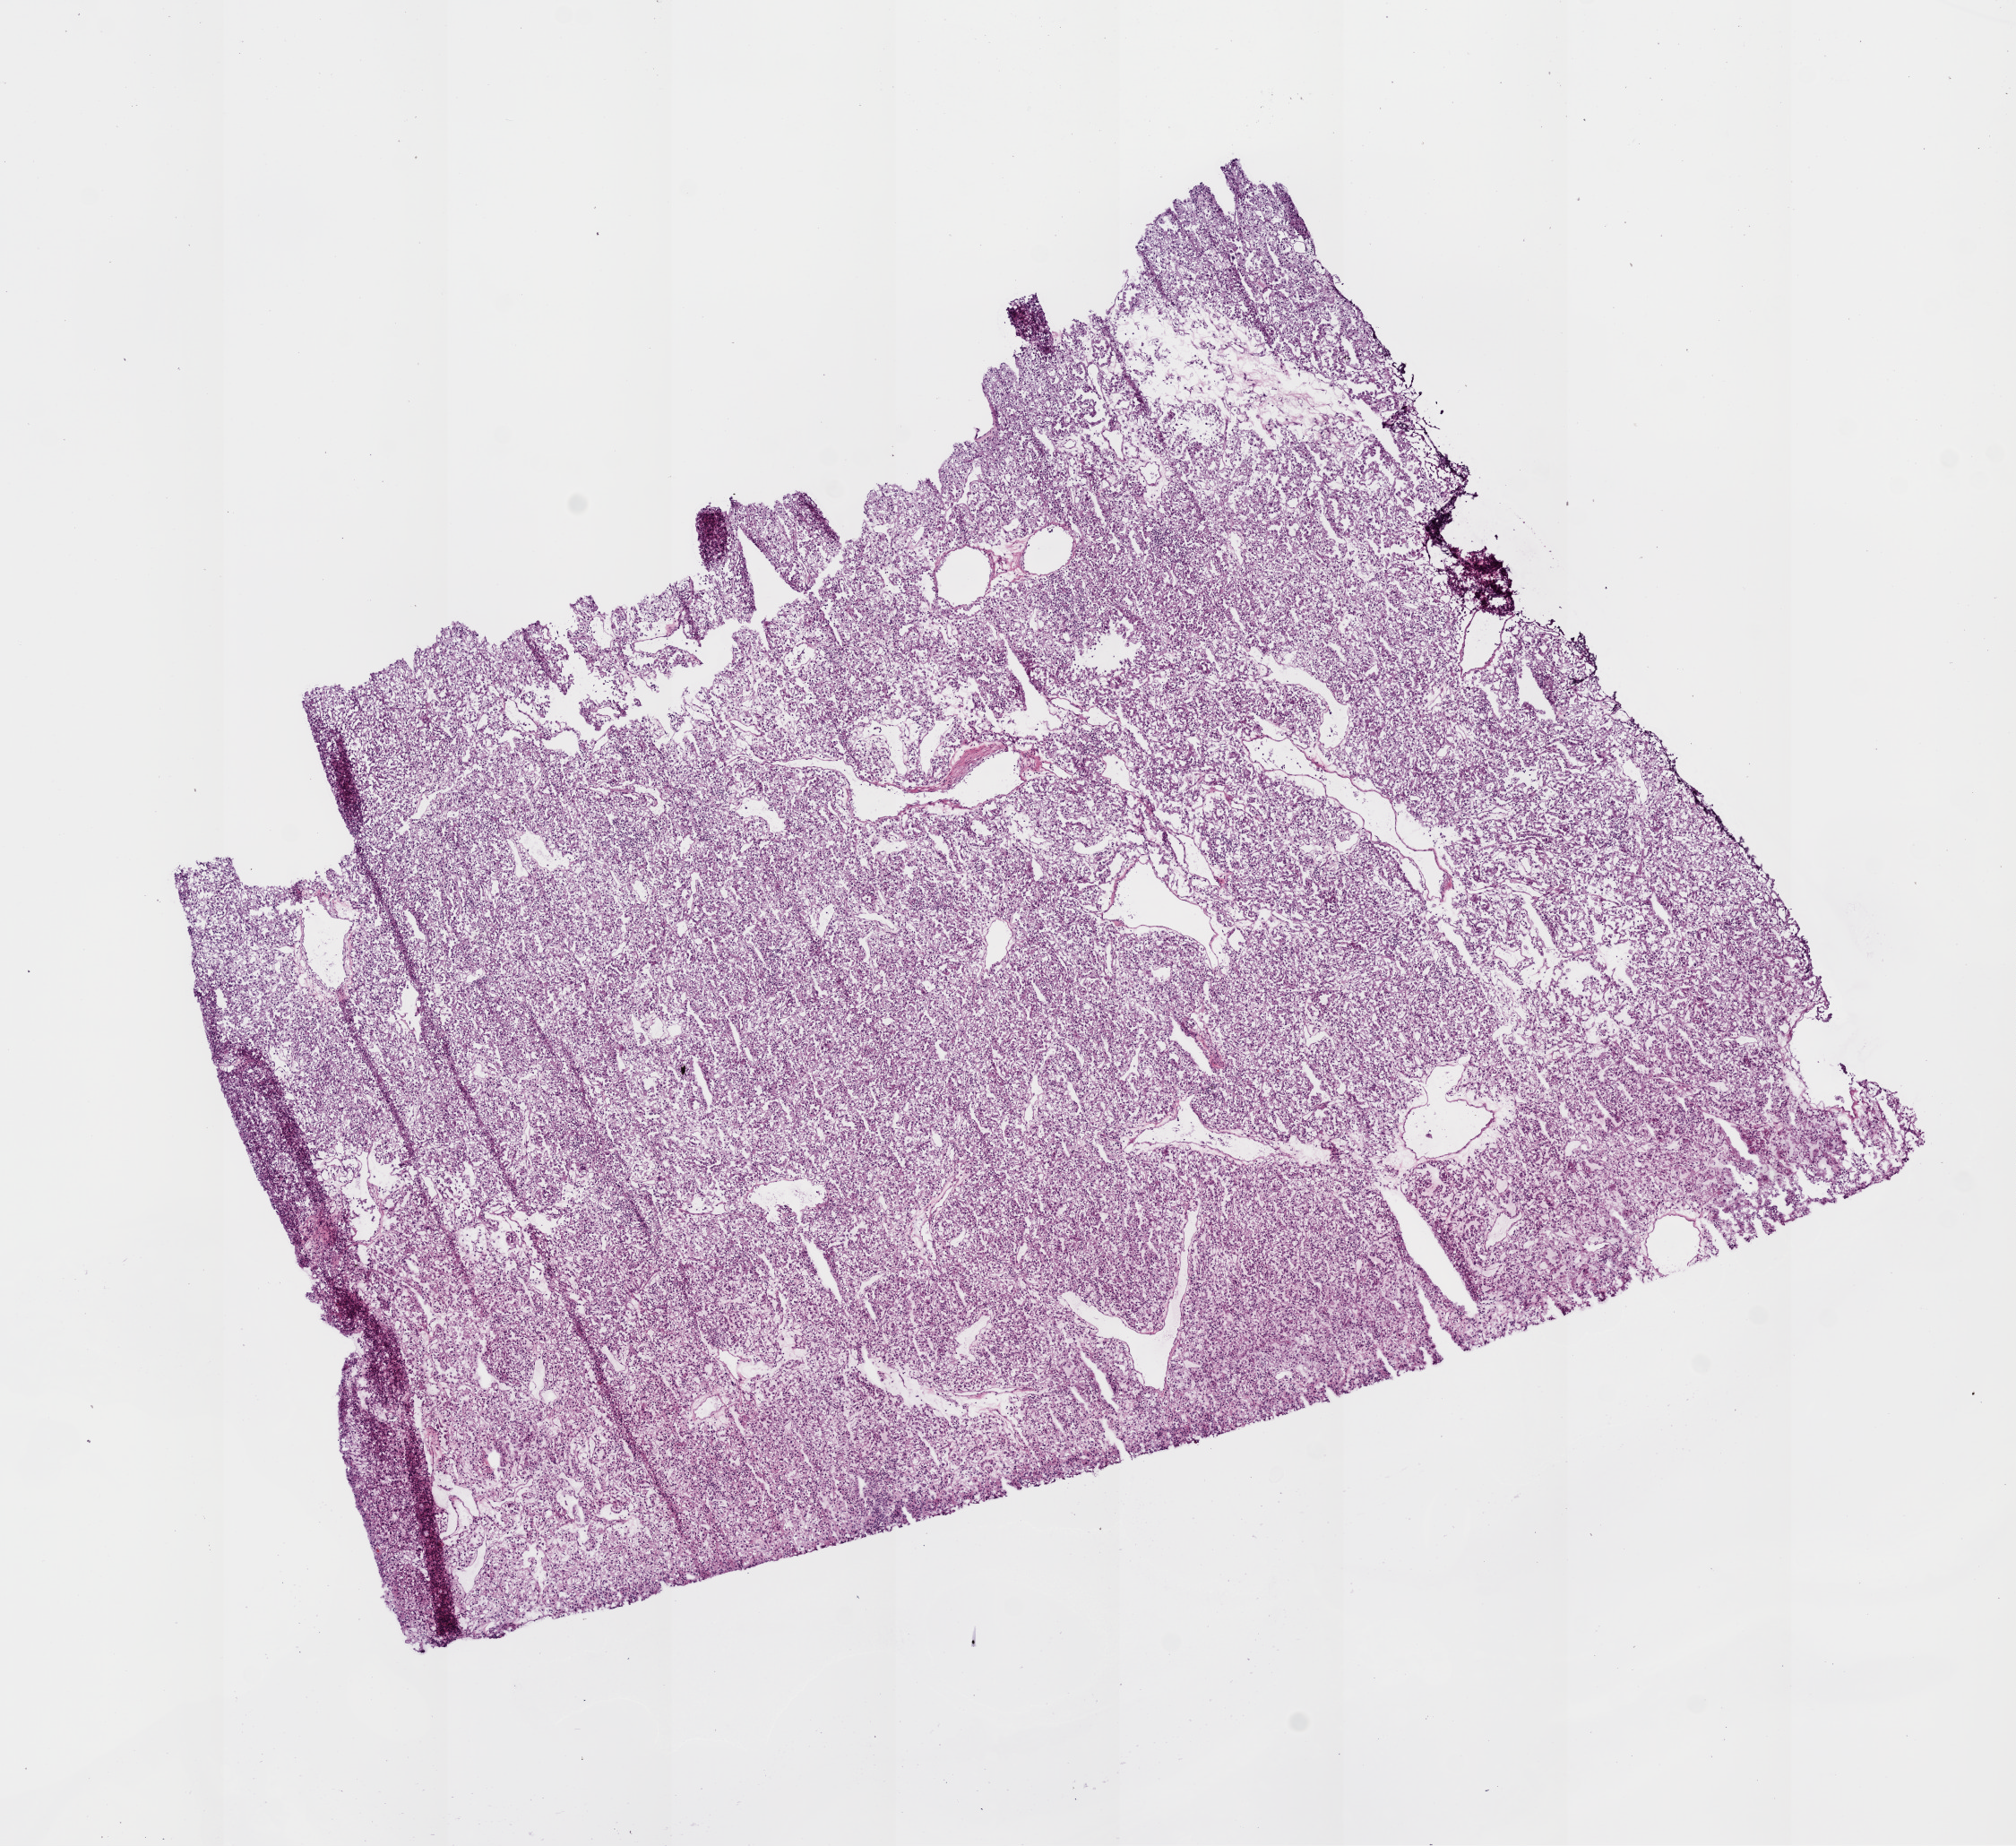
Digitized H&E-stained tissue section (whole slide), whole scanned area (about 9.0 x 8.3 mm, from a 20x scan) shown as a low-resolution overview, frozen section, primary tumour sample from the kidney. Male patient; age at initial diagnosis 44 years. Histologic grade: G3 (poorly differentiated). Composition of this section per pathologist review: tumour cells 95%, tumour nuclei 85%, normal cells 0%, stromal cells 5%, necrosis 0%.
- histologic diagnosis: Clear cell adenocarcinoma, NOS
- laterality: right
- AJCC pathologic stage: I